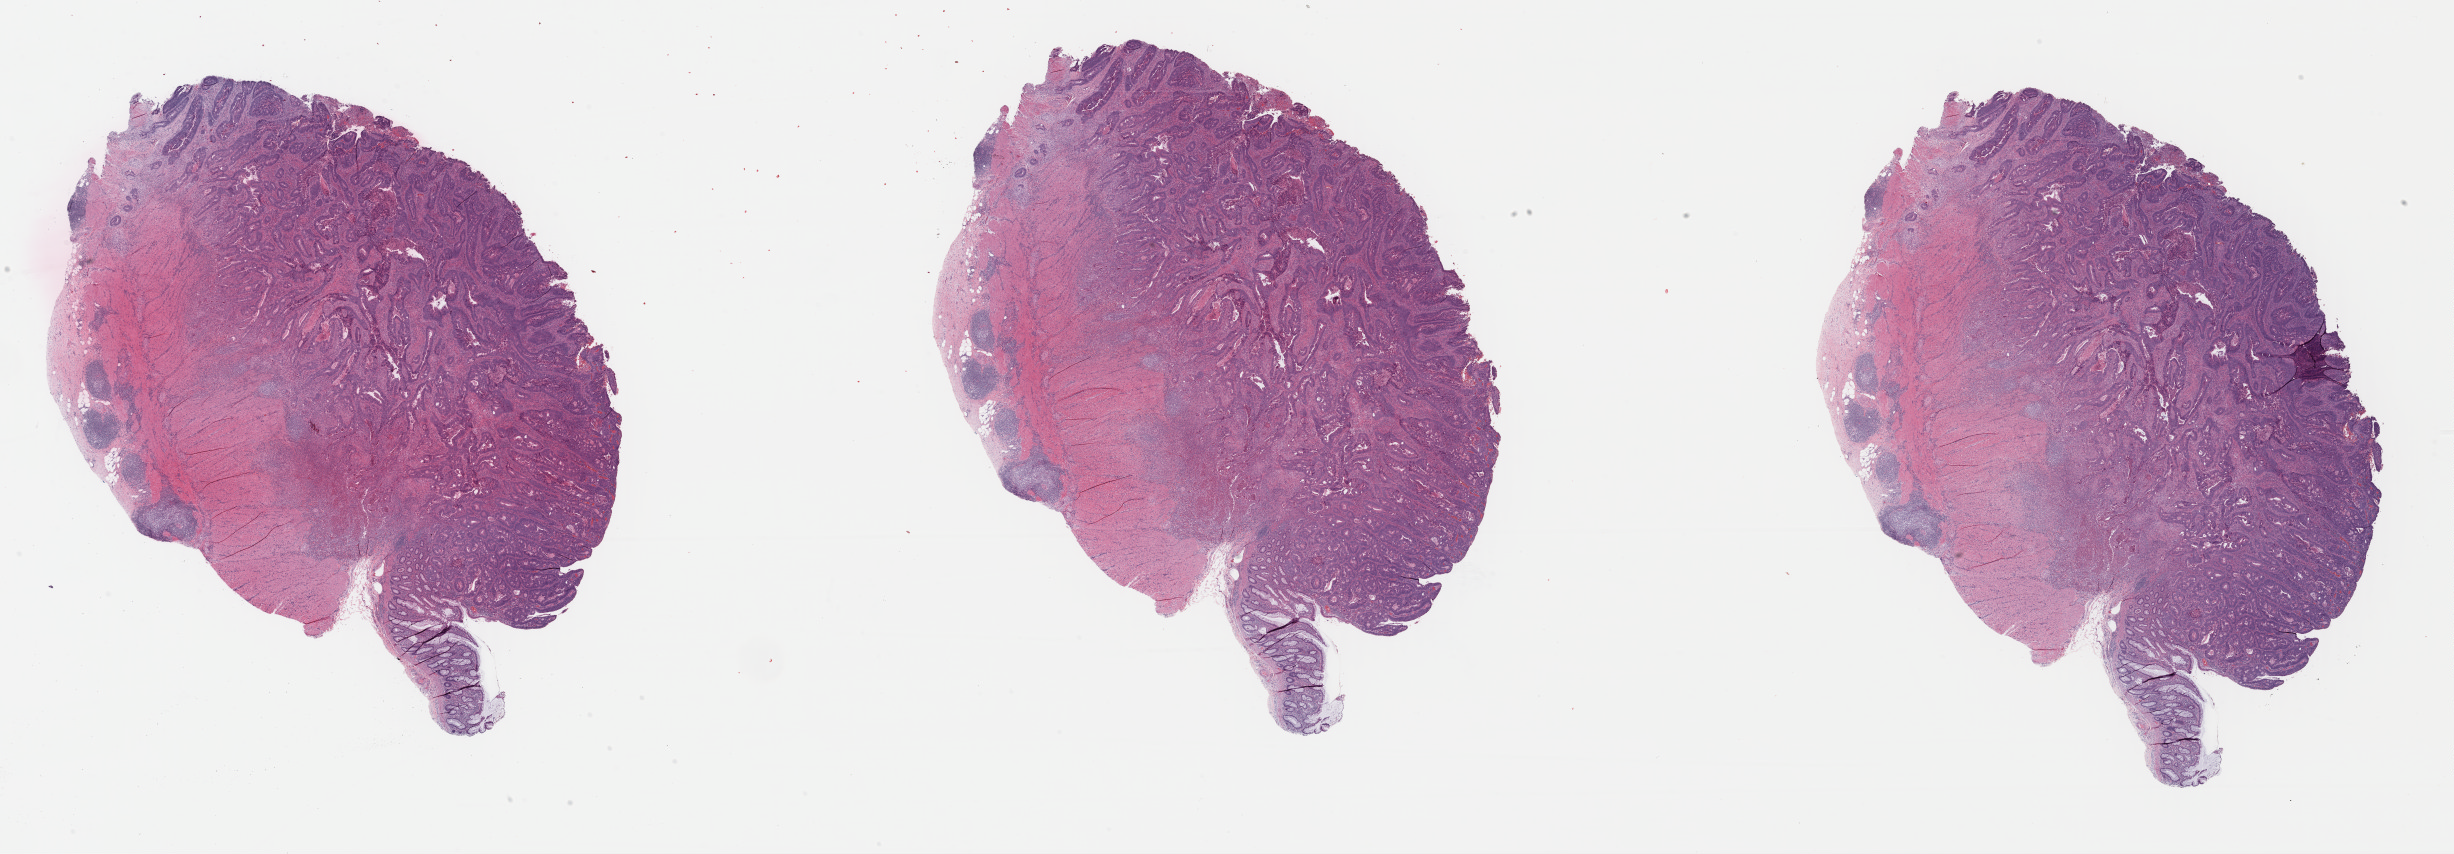
Digitized H&E-stained tissue section (whole slide), a low-resolution overview of the entire scanned area, about 38.6 x 13.4 mm, formalin-fixed paraffin-embedded (FFPE) diagnostic section, sample: primary tumour, rectum. Female, age 48 years at initial diagnosis.
Diagnosis: Adenocarcinoma, NOS (rectosigmoid junction). Lymph nodes positive (case pathology): 10 of 23 examined. AJCC pathologic stage: IIIC (6th edition).